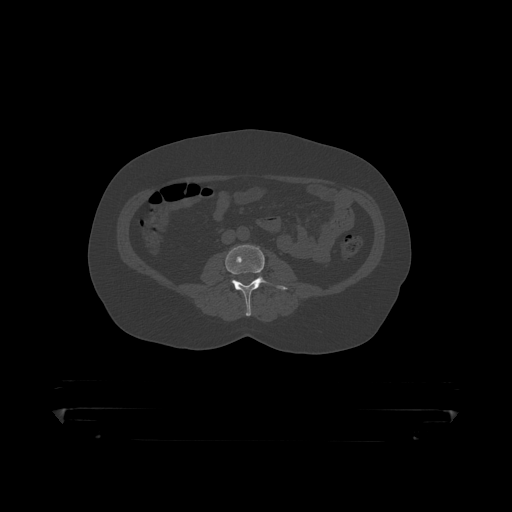
CT including the spine, one axial slice; slice 87 of 390 in the series (ordered by position); reconstruction kernel STANDARD; 120 kVp; bone window (W 1800 / L 400 HU); 1.25 mm slice thickness; 512 × 512 image matrix, field of view 650 × 650 mm. Patient: male, 60 years. Case-level facts recorded for this patient, not image findings: primary cancer: prostate.
Outlined on this slice (semi-automatic segmentation, software-assisted and operator-edited):
- L3 vertebra: bounding box (x1, y1, x2, y2) in pixels: (226, 246, 288, 316)